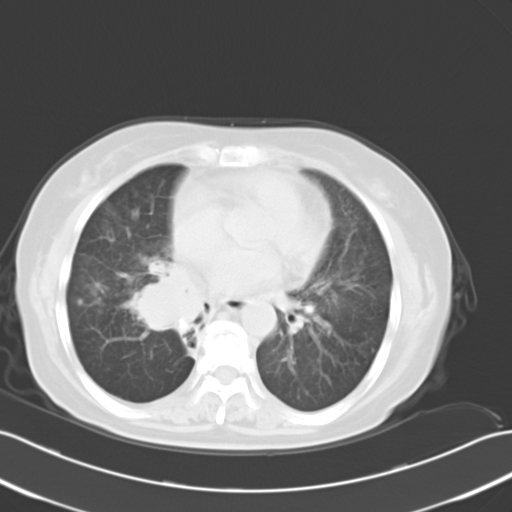
Chest CT, one axial slice; slice 16 of 30 in the series (ordered by position); reconstruction kernel B40f; lung window (W 1500 / L -600 HU); 10 mm slice thickness; 512 × 512 image matrix. Female patient, age 65 years. Case-level facts recorded for this patient, not image findings: clinical TNM (as recorded): T1c N3 M0.
Annotated regions visible in this slice (rectangle marked by the reading radiologist):
- lung tumour (recorded histology: small cell carcinoma): box from (x=139, y=257) to (x=207, y=339) px